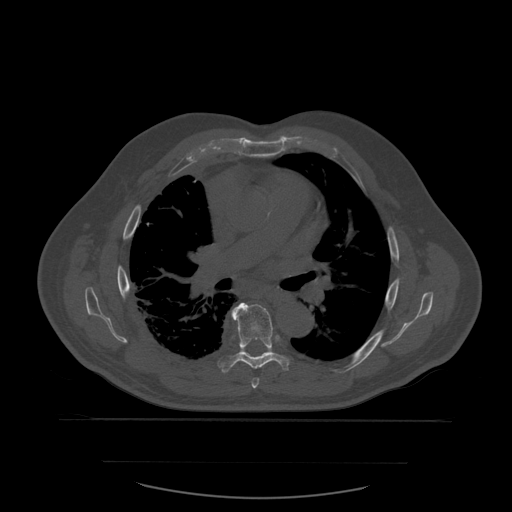
CT including the spine, one axial slice; position 385 of 590 along the scan axis; bone window (W 1800 / L 400 HU); 512 × 512 image matrix, field of view 479 × 479 mm. Patient age 71 years. Case-level facts recorded for this patient, not image findings: primary cancer: lung; vertebrae with lytic lesions (as recorded): T1, T2, L5, S1.
Annotated regions visible in this slice (semi-automatically segmented with operator editing):
- T6 vertebra: box from (x=252, y=378) to (x=260, y=389) px
- T7 vertebra: (x=217, y=303)–(x=294, y=373)